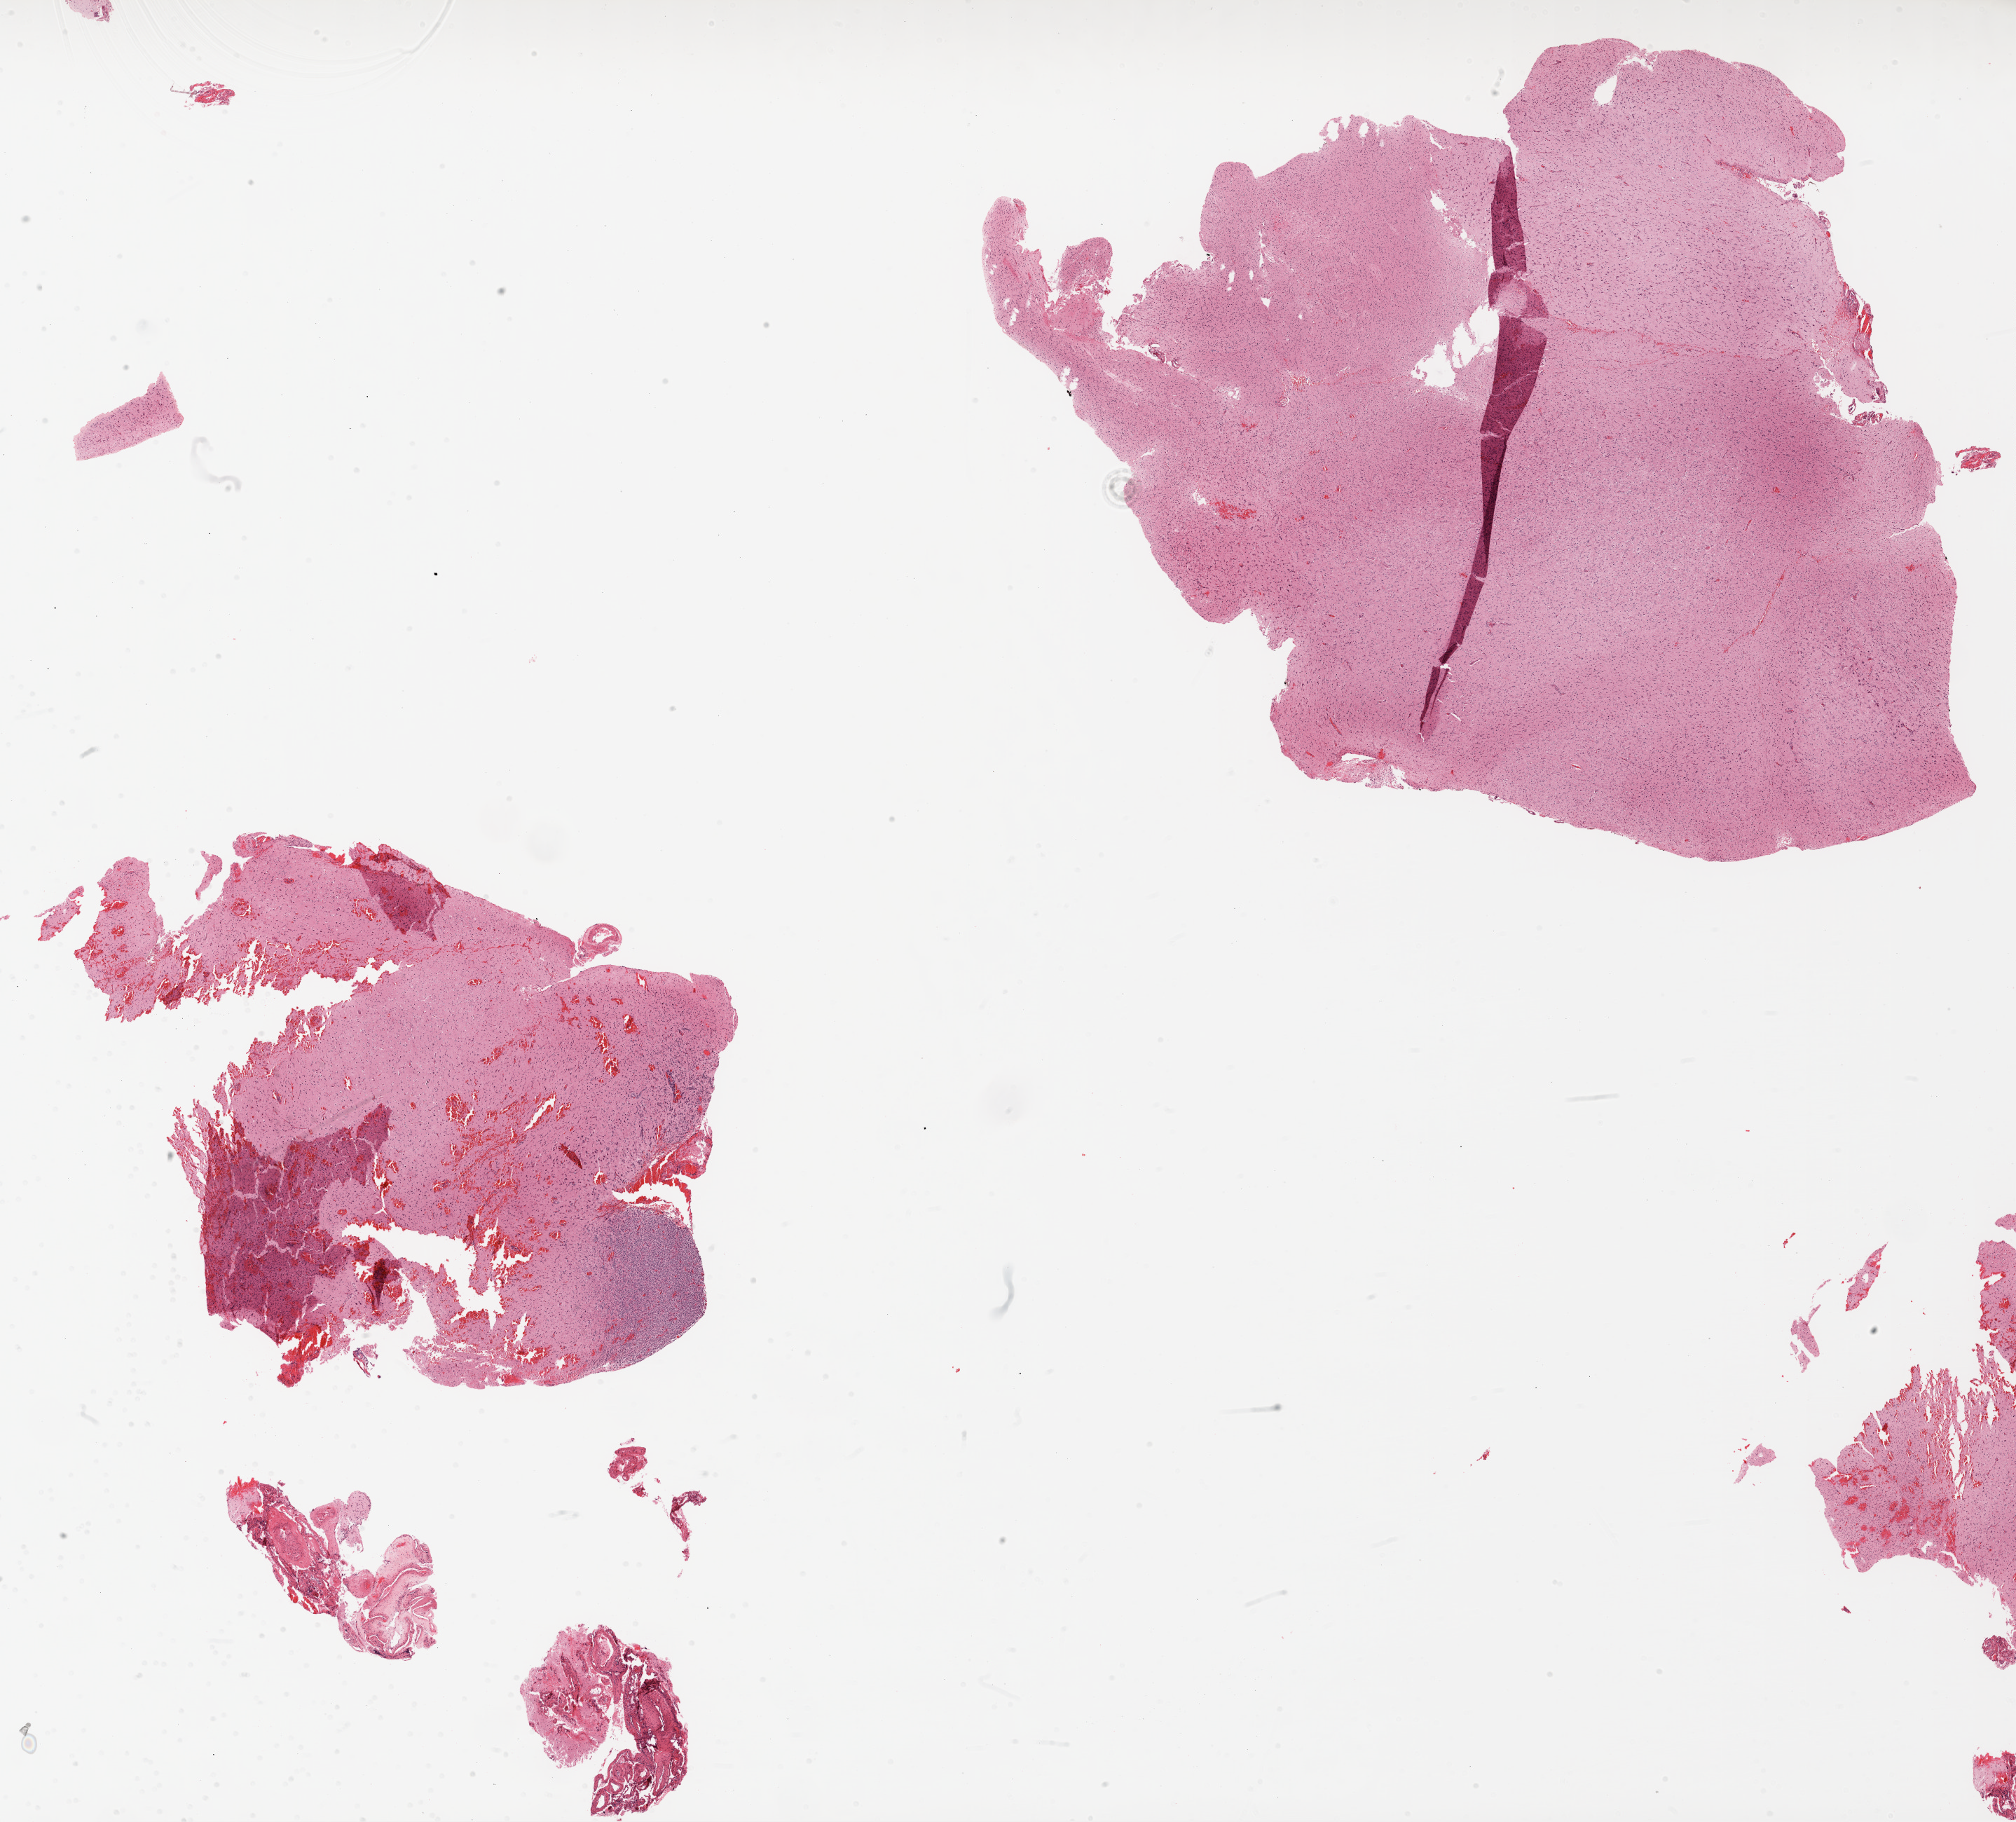
Whole-slide histology image, H&E — whole scanned area (about 23.2 x 21.0 mm) shown as a low-resolution overview. FFPE section. Brain, primary tumour sample. Male, age 65 years at initial diagnosis.
Diagnosis: Glioblastoma.